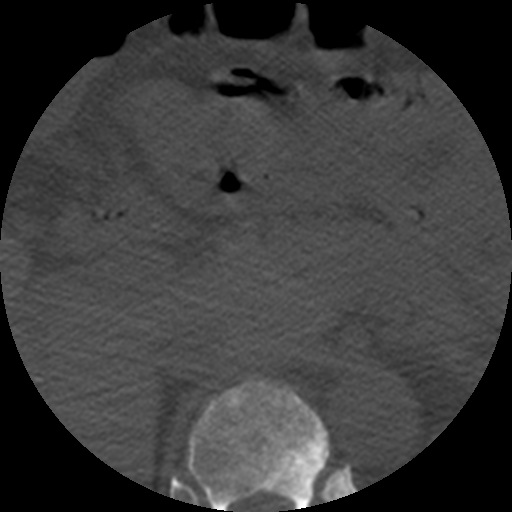
CT including the spine, one axial slice; position 250 of 508 along the scan axis; reconstruction kernel STANDARD; bone window (W 1800 / L 400 HU); 1.25 mm slice thickness; 512 × 512 image matrix, field of view 160 × 160 mm. Patient age 57 years. Case-level facts recorded for this patient, not image findings: primary cancer: prostate.
Annotated regions visible in this slice (semi-automatically segmented with operator editing):
- T11 vertebra: bounding box [x1, y1, x2, y2] px = [187, 376, 330, 512]